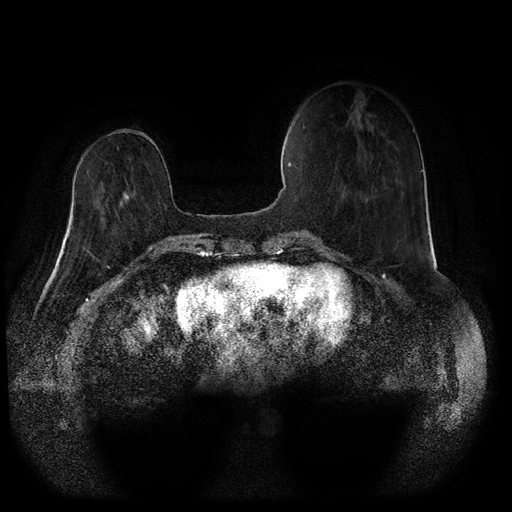
Breast MRI (dynamic contrast-enhanced, multi-phase), one axial slice. Position 23 of 116 along the scan axis. Dynamic contrast-enhanced series, time point 2 of 5 at this slice position (early post-contrast). 1.5 T. TE 2.6 ms, TR 5.3 ms. 2 mm slice thickness. 512 × 512 image matrix. Patient: female, 71 years.
Structures marked on this image (semi-automatic segmentation, software-assisted and operator-edited):
- breast lesion (labelled 'tumour' in the annotation; benign lesions carry a separate 'benign' label): bounding box [x1, y1, x2, y2] px = [120, 193, 129, 206]